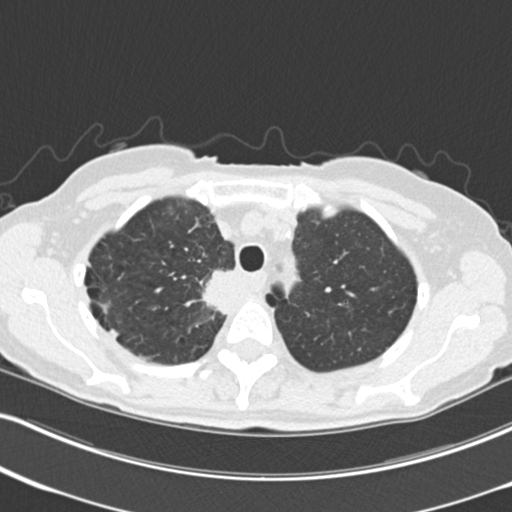
Axial slice from a low-dose chest CT screening exam, third annual screen, lung window (W 1500 / L -600 HU), 2 mm slice thickness, standard (soft-tissue) reconstruction kernel (B30f), slice 48 of 226 in the series, 512 × 512 image matrix. Female participant, aged 68 years at enrolment. Current smoker at enrolment.
Expert reader's lesion annotation, box from (x=199, y=264) to (x=251, y=319) px. Screening reader's record for this exam (one nodule recorded; not confirmed to be the boxed lesion): non-calcified nodule or mass ≥4 mm, right upper lobe, 31 × 29 mm, poorly defined margins, soft tissue attenuation, pre-existing on the prior screen: no. Official screen result: positive, other. Lung cancer was diagnosed 79 days after this screen: squamous cell carcinoma, NOS, right upper lobe, mediastinum, poorly differentiated (G3), stage IIIB (AJCC 6th edition), 43 mm at pathology.